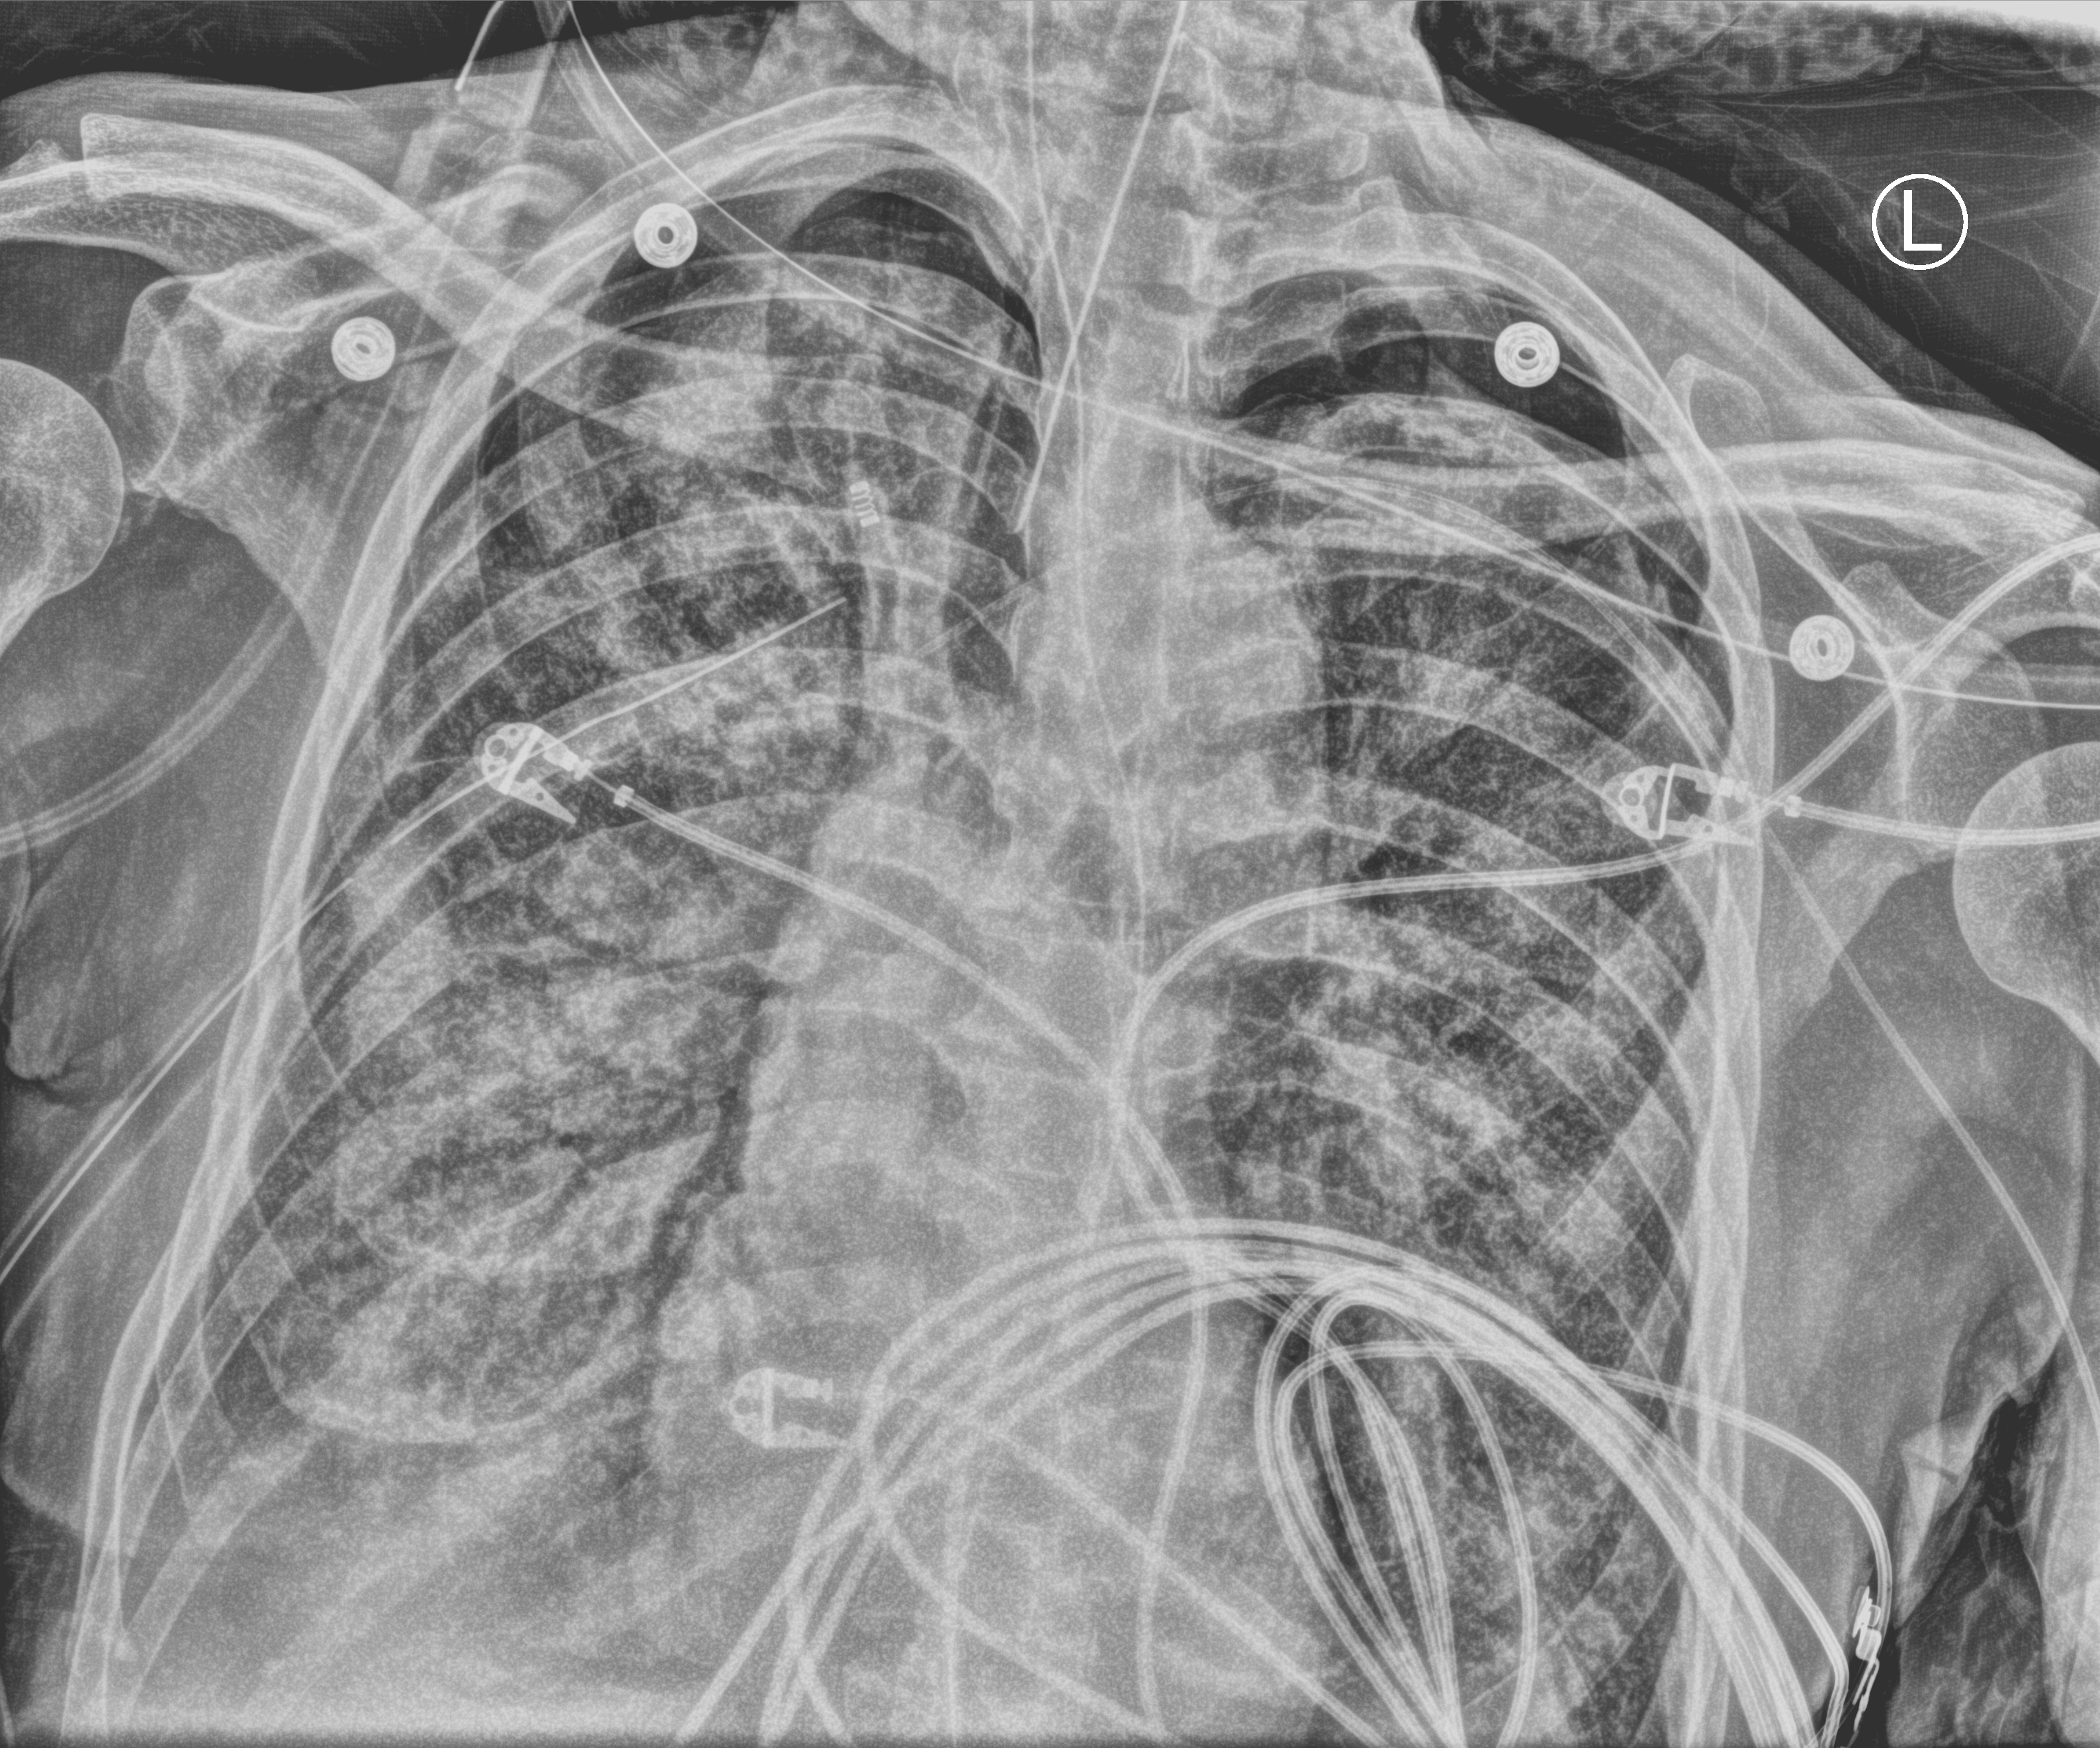
Chest X-ray (portable), anteroposterior (AP) projection. Male patient hospitalised with COVID-19, age 60–74 years.
From the hospital-stay record, not from the radiograph (when in the stay this image was taken is not recorded): mechanically ventilated during this hospital stay: yes.